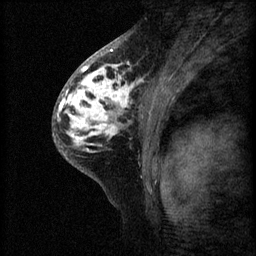
Breast MRI (dynamic contrast-enhanced), one sagittal slice. Slice 38 of 60 in the series (ordered by position). 3 images stored at this slice position (order not interpretable as contrast timing). 1.5 T. TE 4.2 ms, TR 8.2 ms. 2 mm slice thickness. 256 × 256 image matrix. Female patient, age 41 years.
Outlined on this slice (semi-automatic segmentation, software-assisted and operator-edited):
- analysis volume of interest (the breast-tissue region the enhancement analysis was run in; not a lesion): box from (x=53, y=62) to (x=159, y=175) px
- tumour enhancement mask (voxels above the 70 % enhancement threshold inside the analysis volume of interest): (x=57, y=64)–(x=143, y=153)